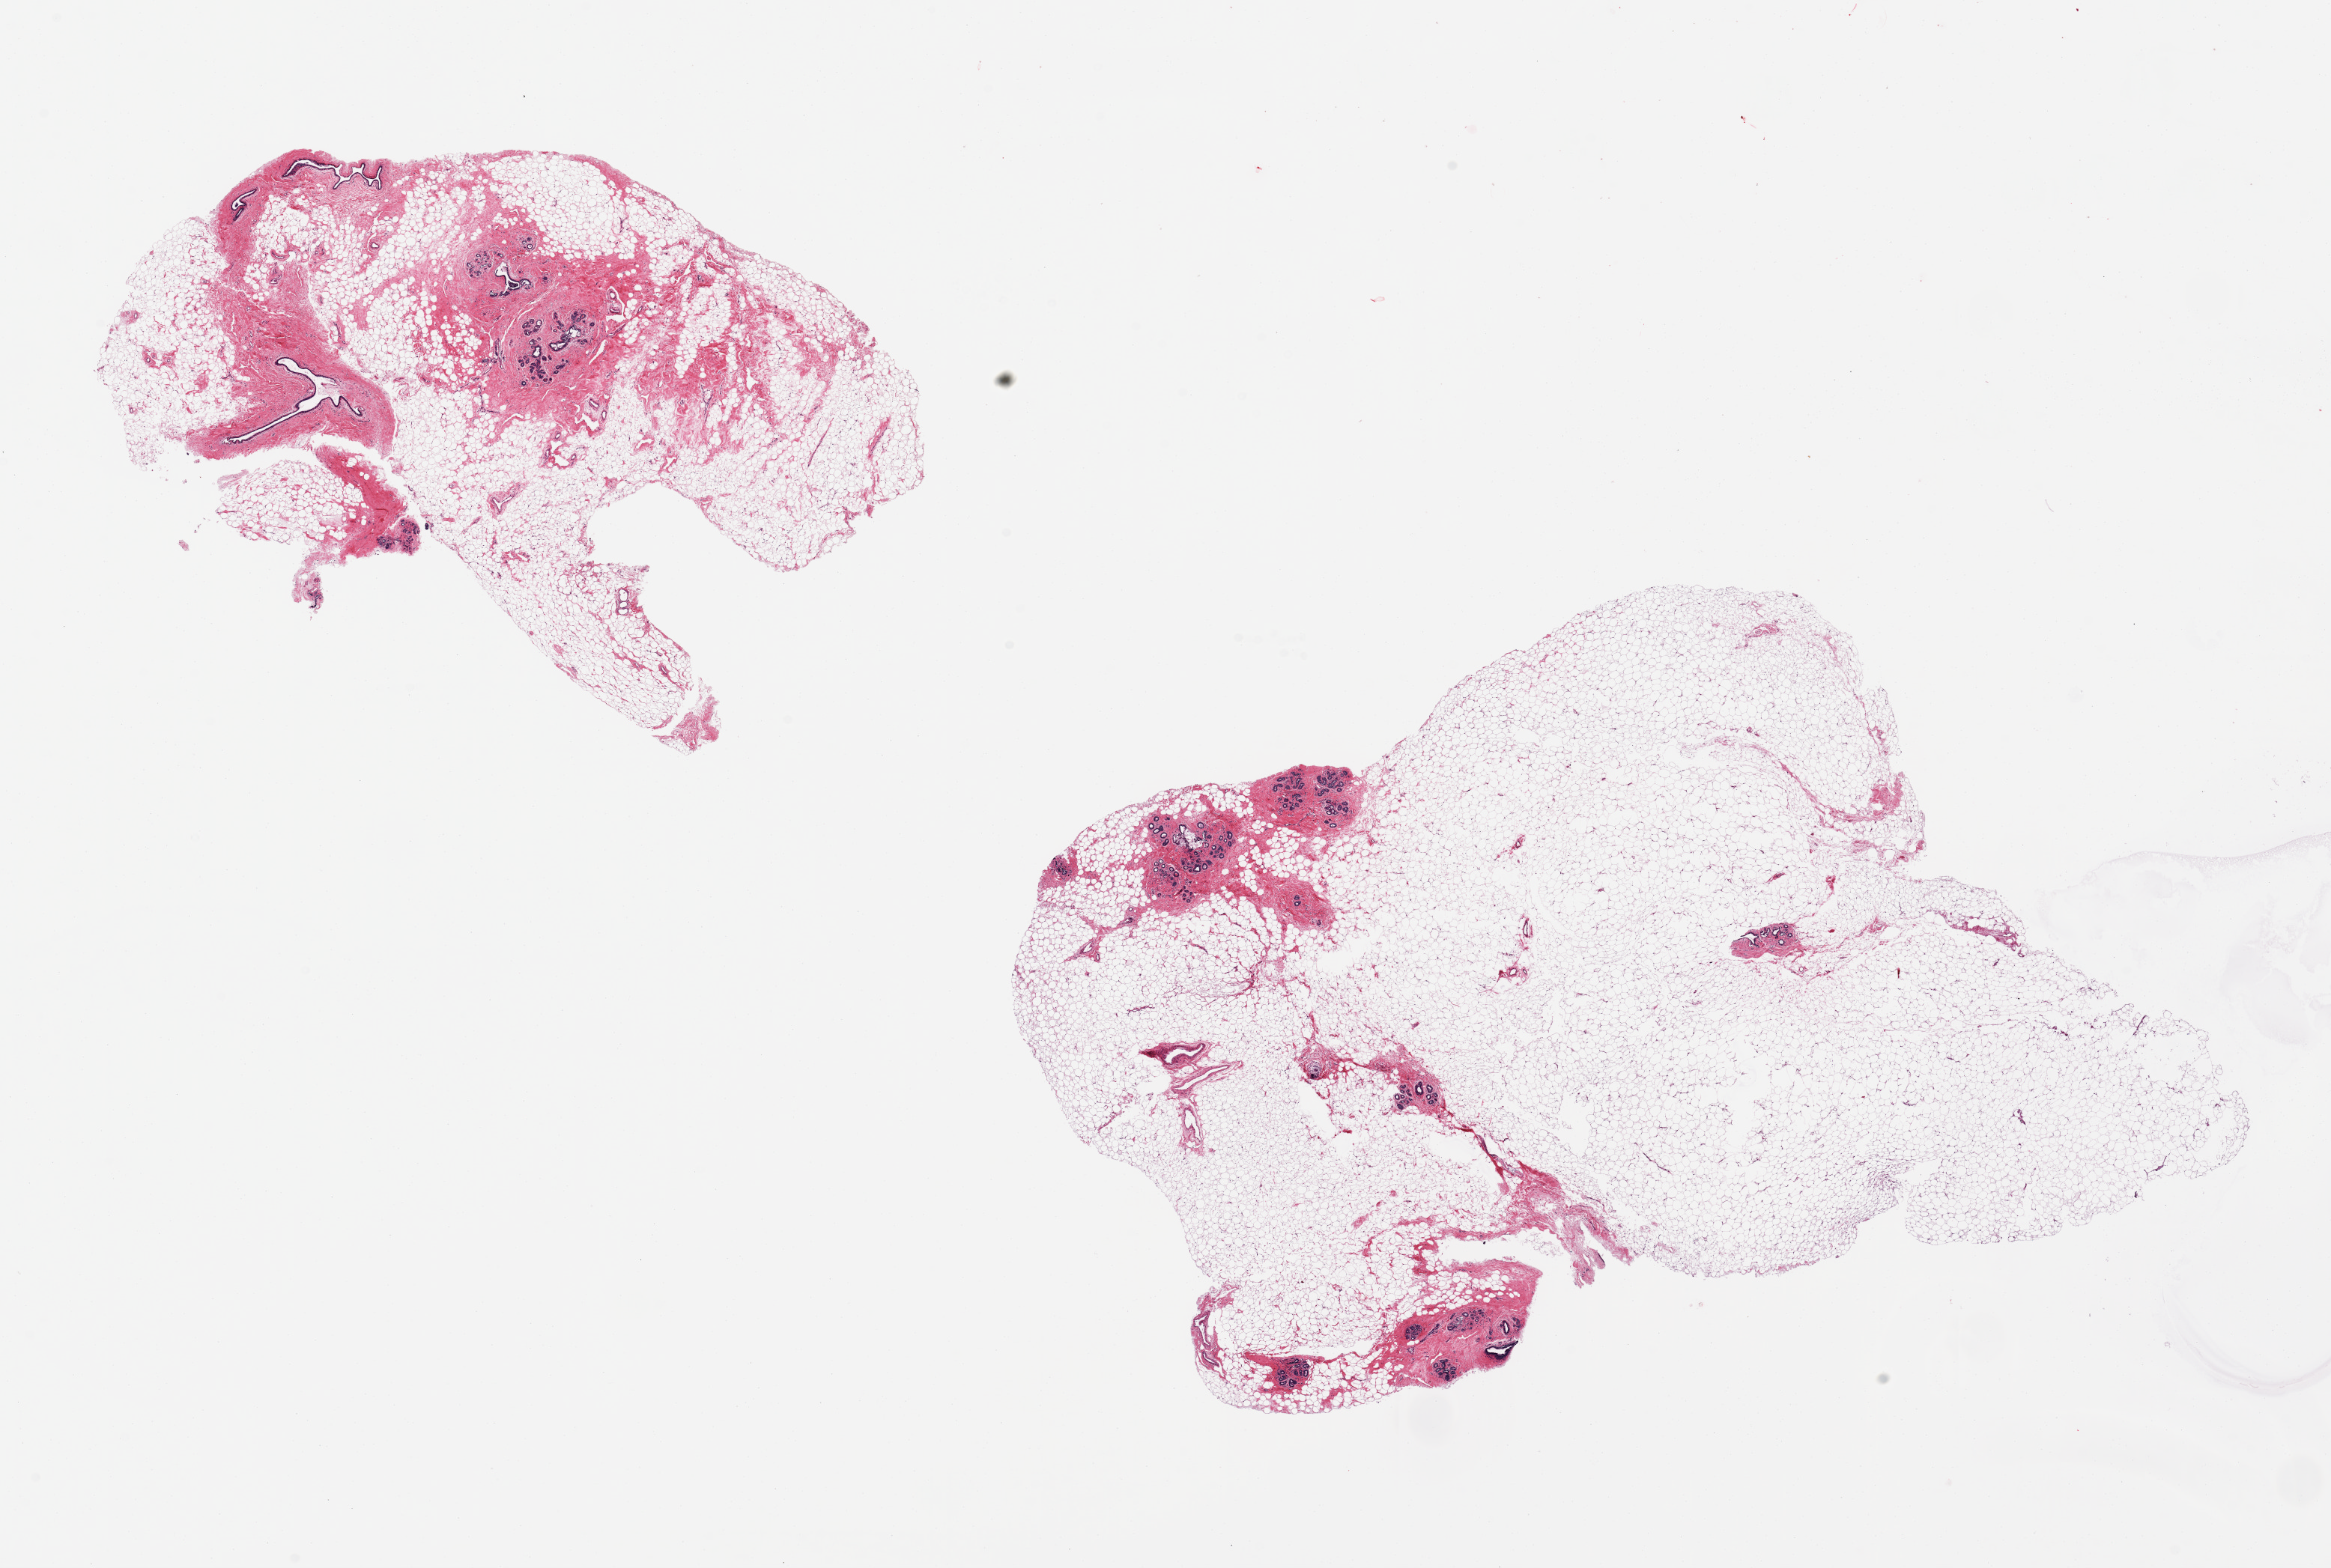
Digitized haematoxylin and eosin-stained section — a low-resolution overview of the entire scanned area, about 24.6 x 16.6 mm (slide scanned at 20x); PAXgene-fixed, paraffin-embedded tissue; section of breast (target tissue); tissue donor sample. Donor sex: female.
Review note (as recorded): 2 ~9x8mm; ducts and lobules; abundant fat 75-90%.